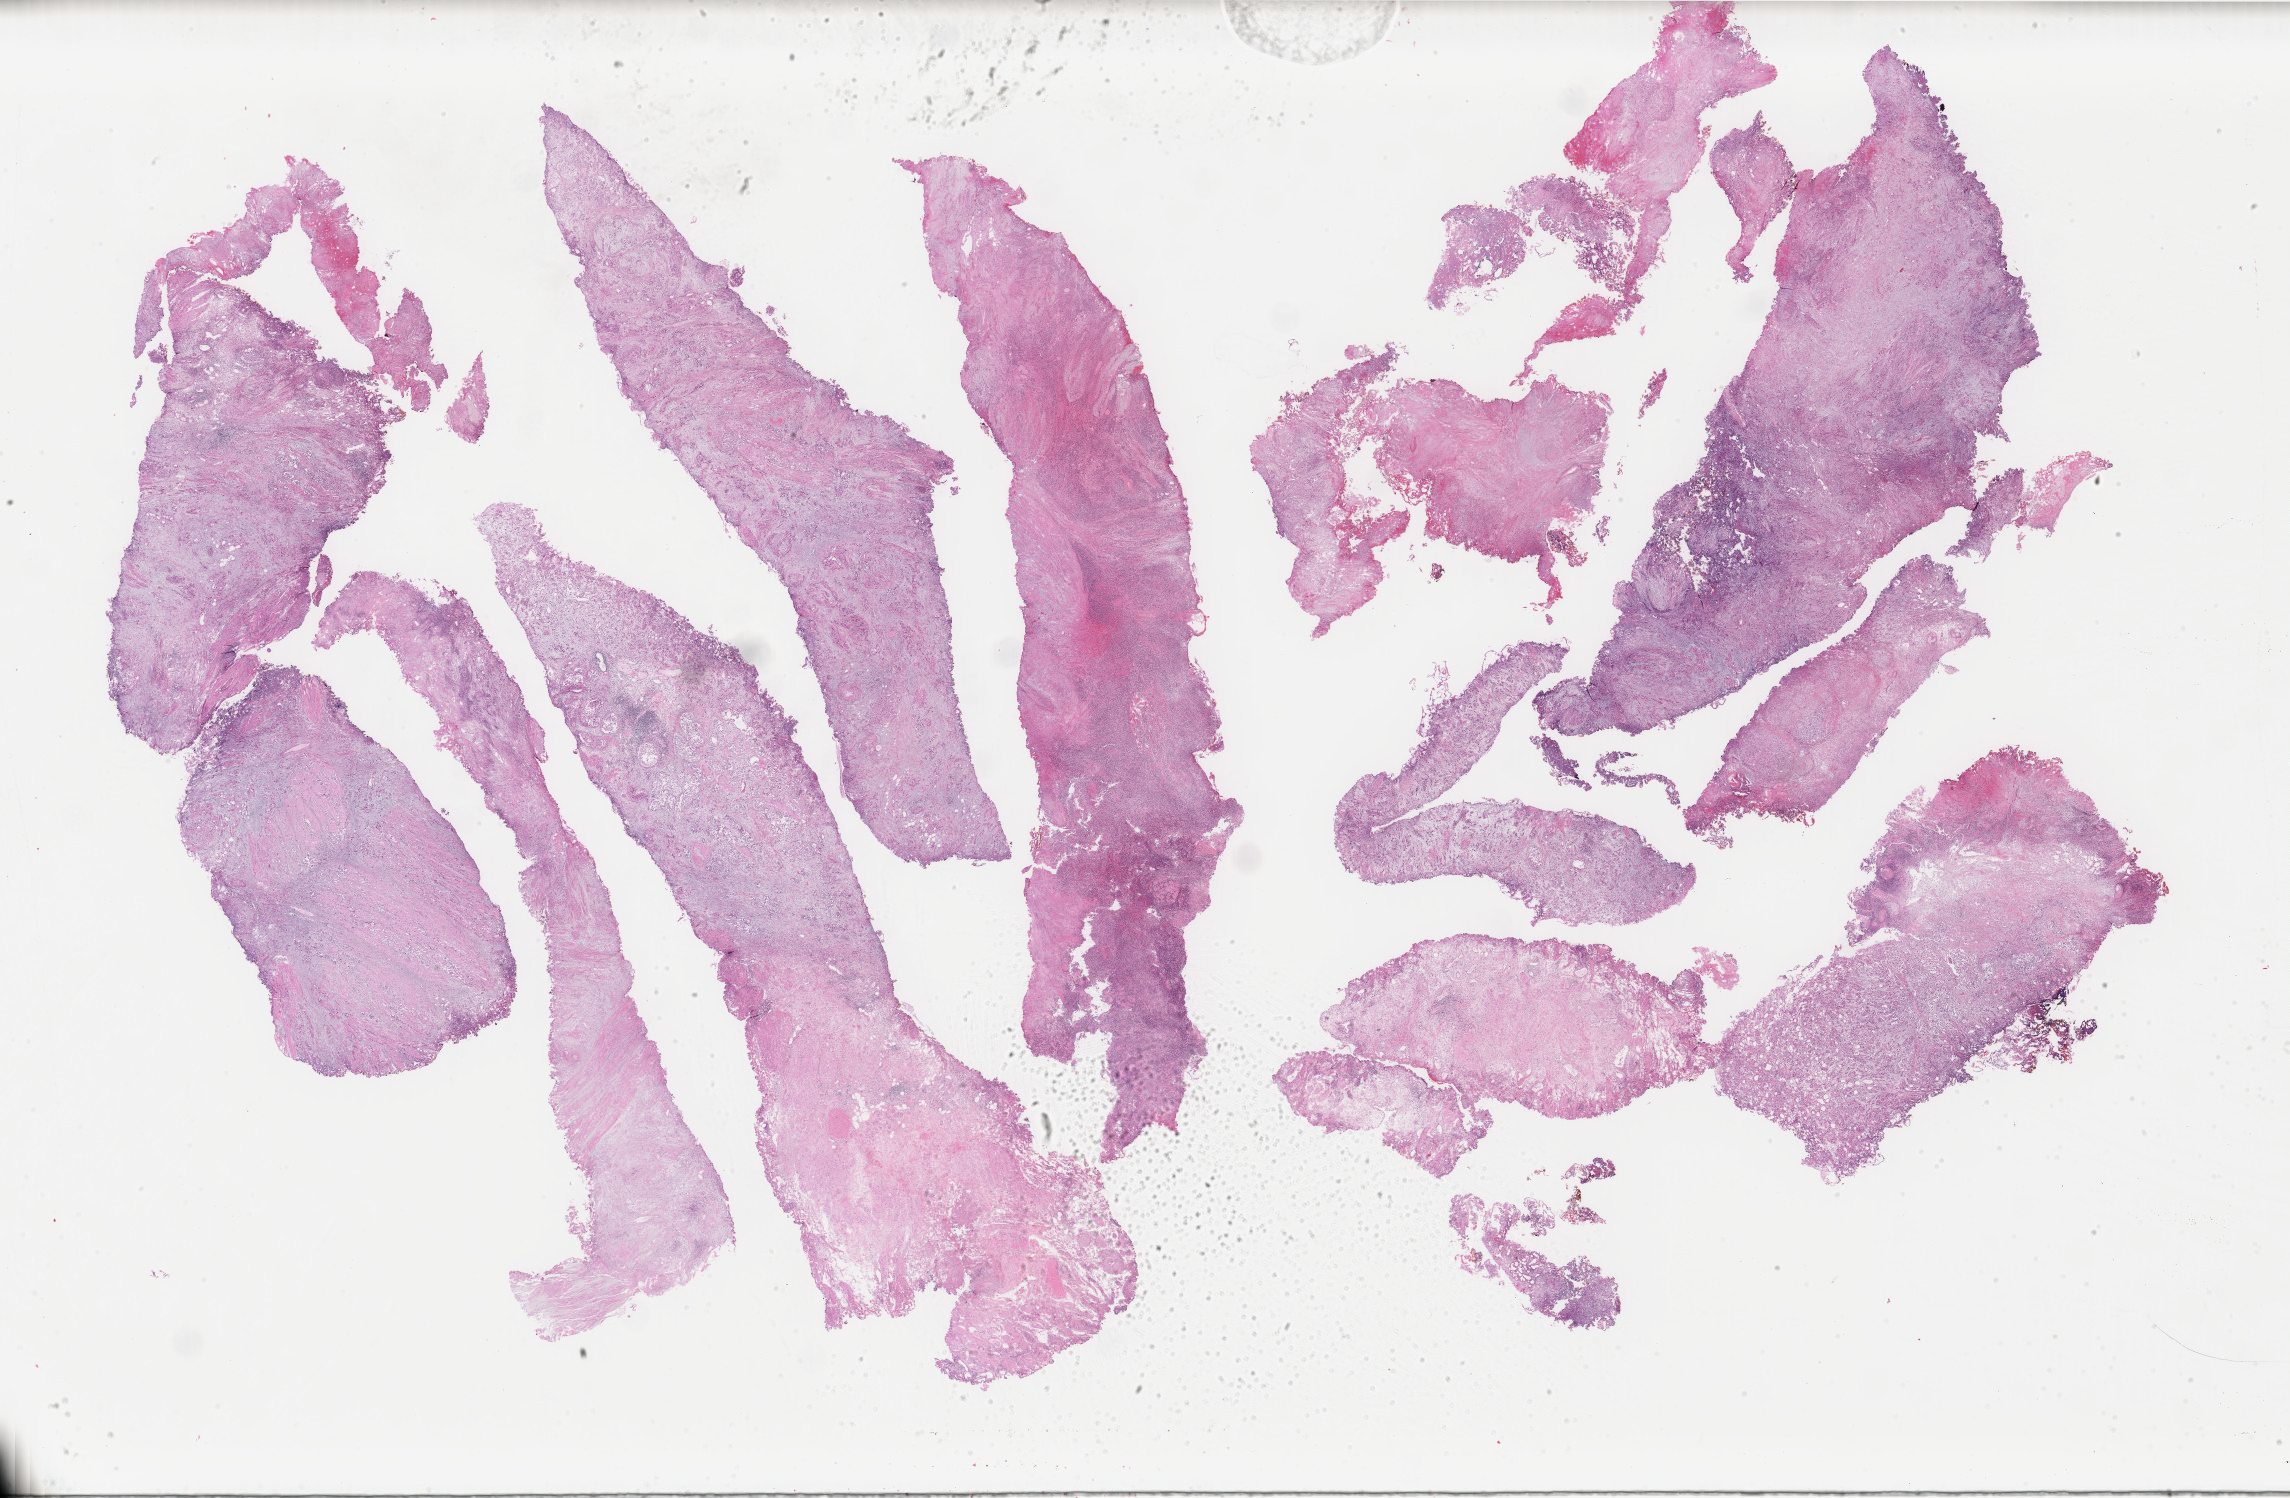
H&E whole-slide image, whole scanned area (about 36.4 x 23.8 mm, slide scanned at 40x) shown as a low-resolution overview. Formalin-fixed paraffin-embedded (FFPE) diagnostic section. Sample: primary tumour, bladder. Patient: female, age at initial diagnosis 58 years.
Diagnosis: Transitional cell carcinoma.